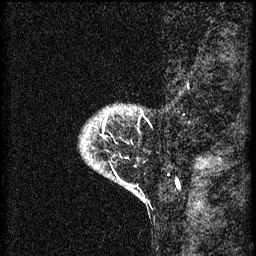
Breast MRI (dynamic contrast-enhanced), one sagittal slice; position 8 of 60 along the scan axis; 3 images stored at this slice position (order not interpretable as contrast timing); 1.5 T; TE 4.2 ms, TR 8.2 ms; 256 × 256 image matrix, field of view 180 × 180 mm. Female patient, age 41 years.
Structures marked on this image (semi-automatically segmented with operator editing):
- analysis volume of interest (the breast-tissue region the enhancement analysis was run in; not a lesion): box from (x=83, y=108) to (x=148, y=175) px
- tumour enhancement mask (voxels above the 70 % enhancement threshold inside the analysis volume of interest): (x=105, y=120)–(x=107, y=123)